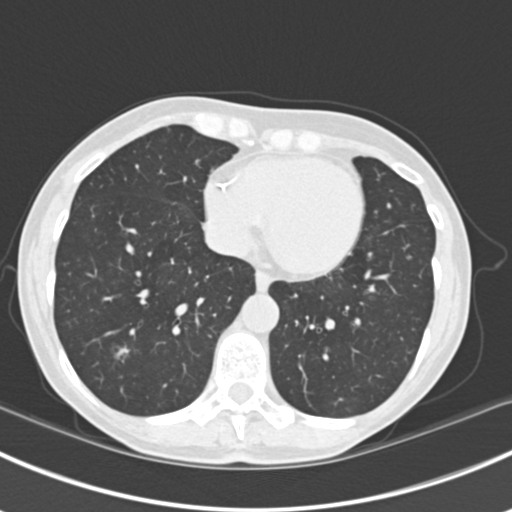
Low-dose screening chest CT, axial slice, baseline annual screen, lung window (W 1500 / L -600 HU), standard (soft-tissue) reconstruction kernel (B30f), 120 kVp, slice 132 of 224 in the series. Female, age 63 years at enrolment. Current smoker at enrolment.
- Expert-annotated lung lesion, box from (x=96, y=319) to (x=147, y=368) px.
- The screening reader recorded 10 non-calcified nodules or masses ≥4 mm on this exam (right lower lobe, right lower lobe, left lower lobe, left lower lobe, right middle lobe, right lower lobe, left lower lobe, left upper lobe, right upper lobe, left upper lobe); which of them this box marks is not recorded.
- Lung cancer was diagnosed 751 days after this screen (after the third annual screen): bronchiolo-alveolar adenocarcinoma, NOS, right upper lobe, right middle lobe, right lower lobe, left upper lobe, left lower lobe, moderately differentiated (G2), stage IV (AJCC 6th edition).